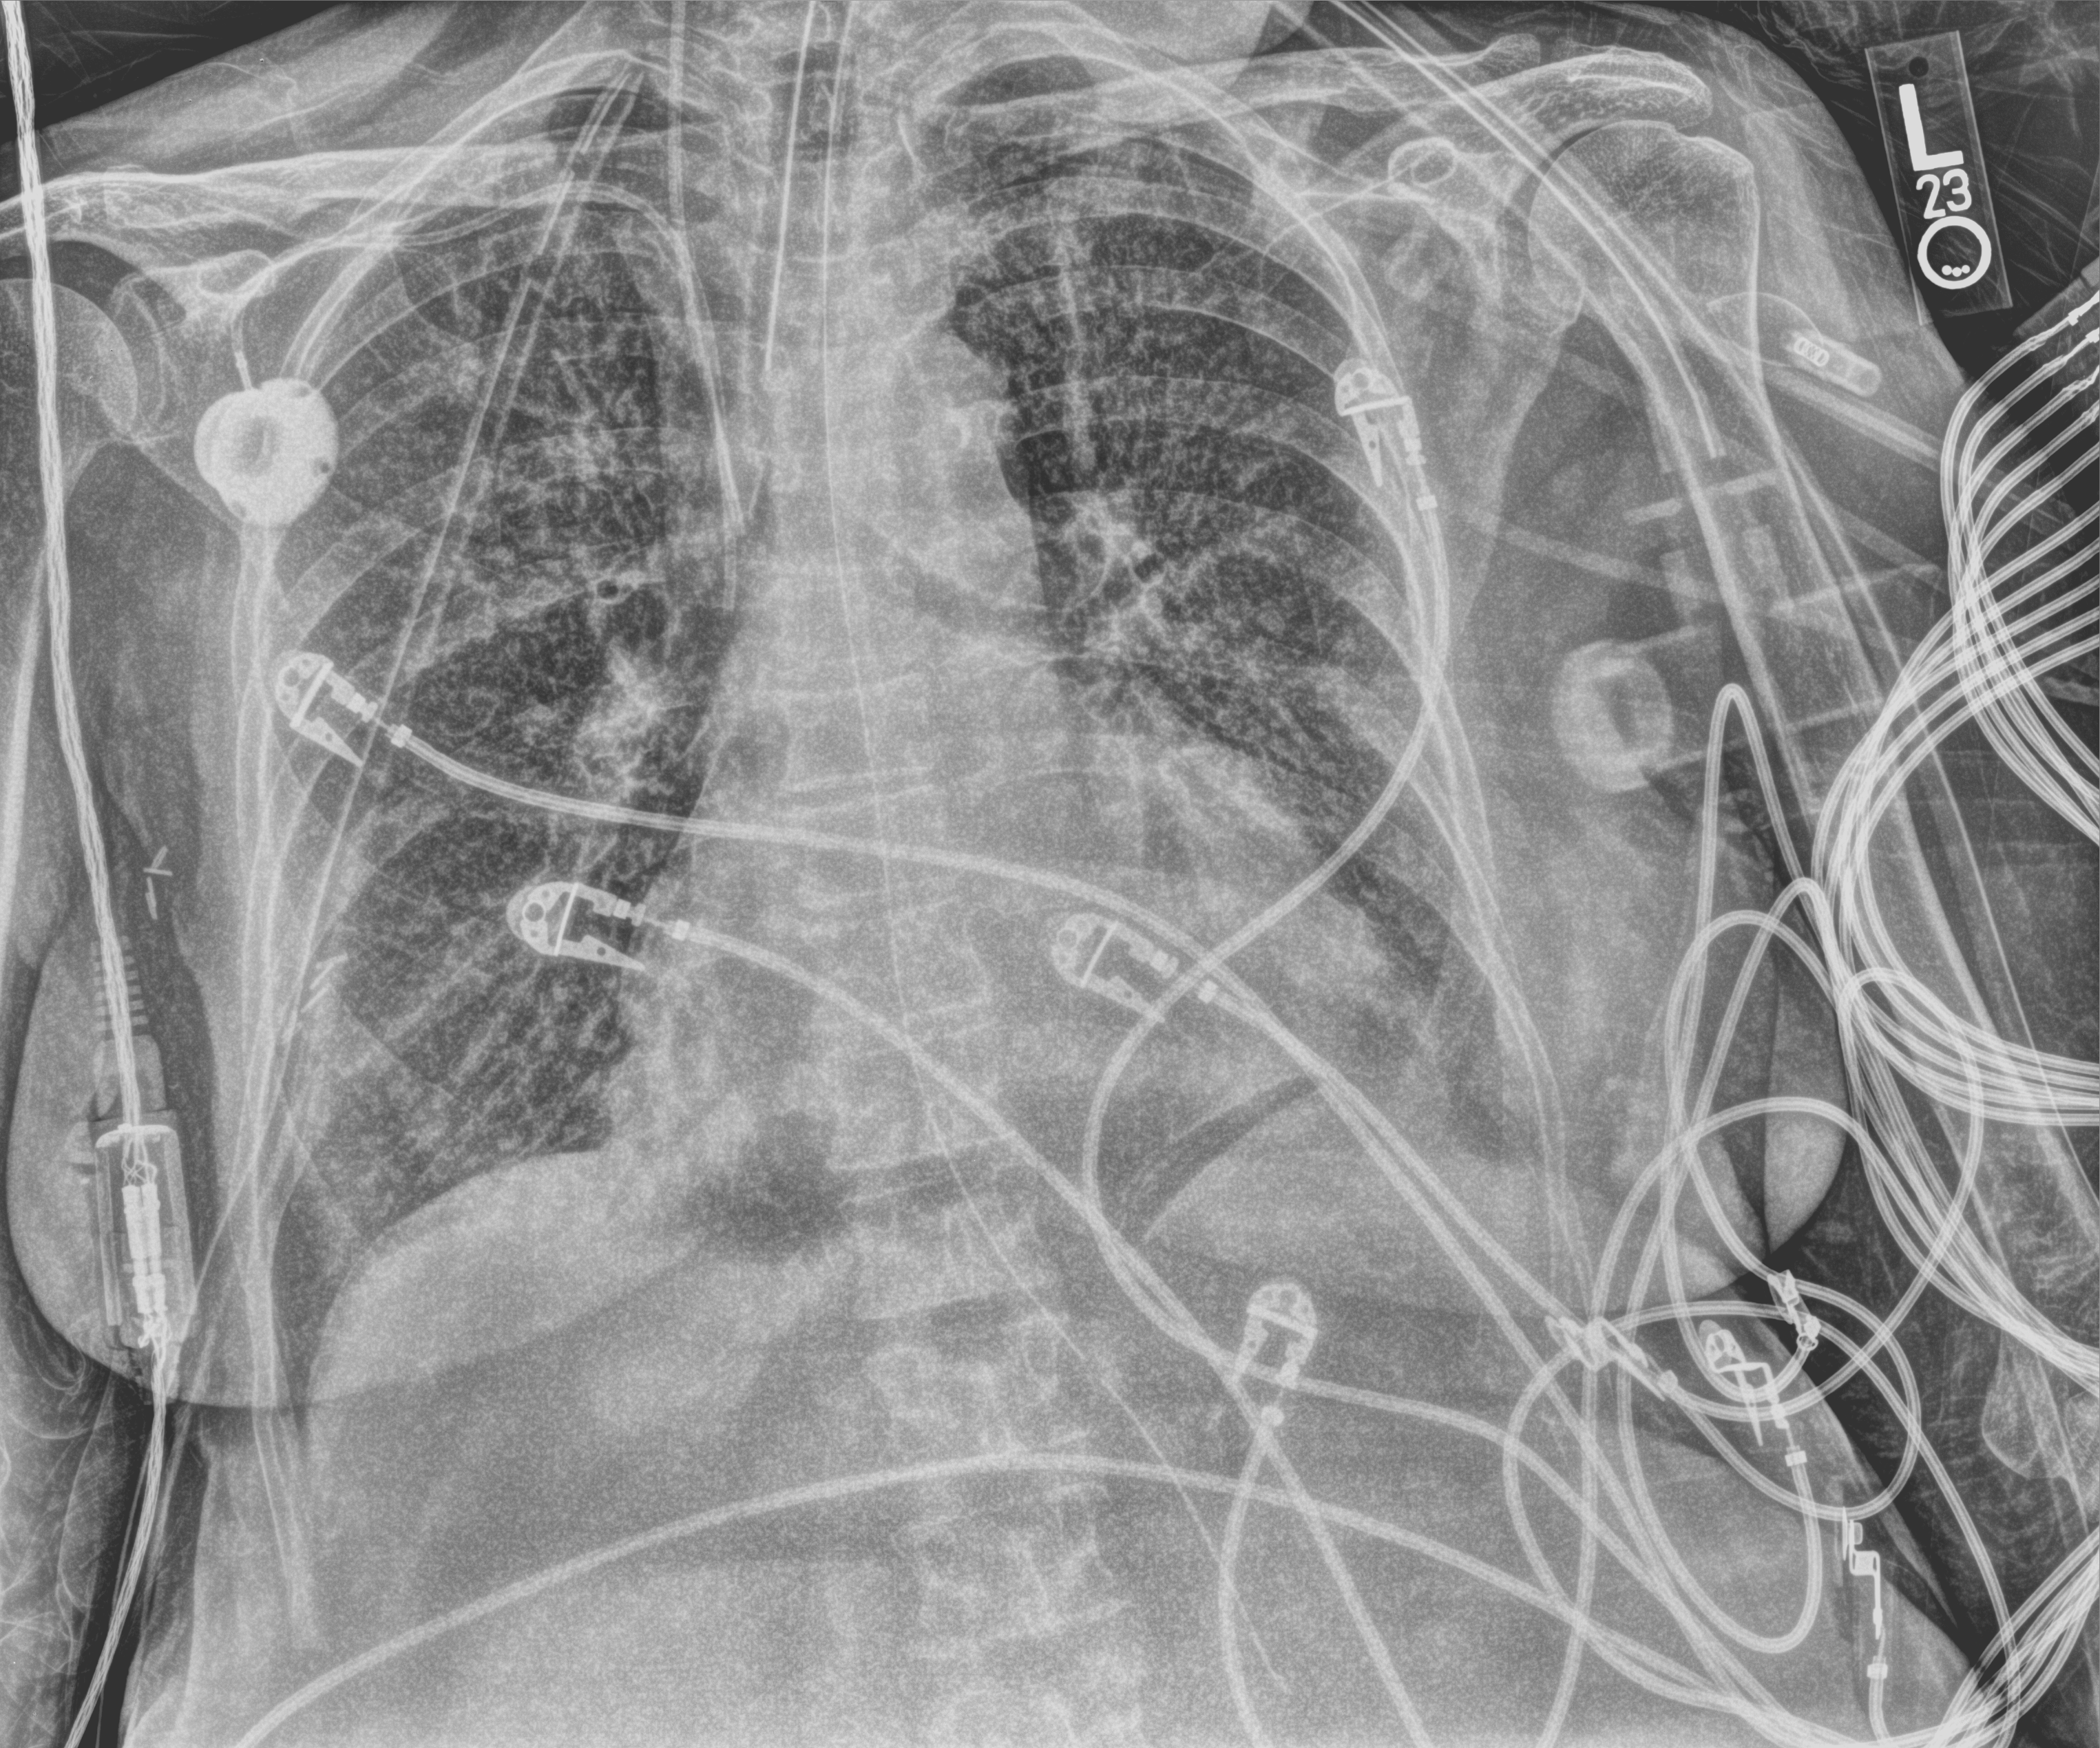
Portable chest radiograph; anteroposterior (AP) projection. Female patient hospitalised with COVID-19, age 60–74 years.
Admission-level facts for this patient (not findings on this image; timing relative to this image not recorded):
- mechanically ventilated during this hospital stay: yes
- other chronic lung disease (admission record): no
- length of hospital stay: 43 days